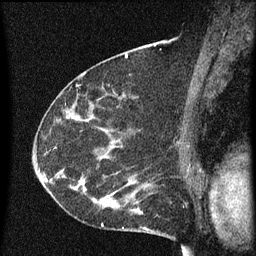
Breast MRI (dynamic contrast-enhanced), one sagittal slice; position 38 of 60 along the scan axis; dynamic contrast-enhanced series, image 2 of 3 at this slice position (ordered by acquisition); 1.5 T; TE 4.2 ms, TR 8 ms; 256 × 256 image matrix, field of view 180 × 180 mm. Patient: female, 55 years.
Outlined on this slice (semi-automatic segmentation, software-assisted and operator-edited):
- analysis volume of interest (the breast-tissue region the enhancement analysis was run in; not a lesion): bounding box (x1, y1, x2, y2) in pixels: (51, 156, 145, 217)
- tumour enhancement mask (voxels above the 70 % enhancement threshold inside the analysis volume of interest): (75, 156, 139, 215)